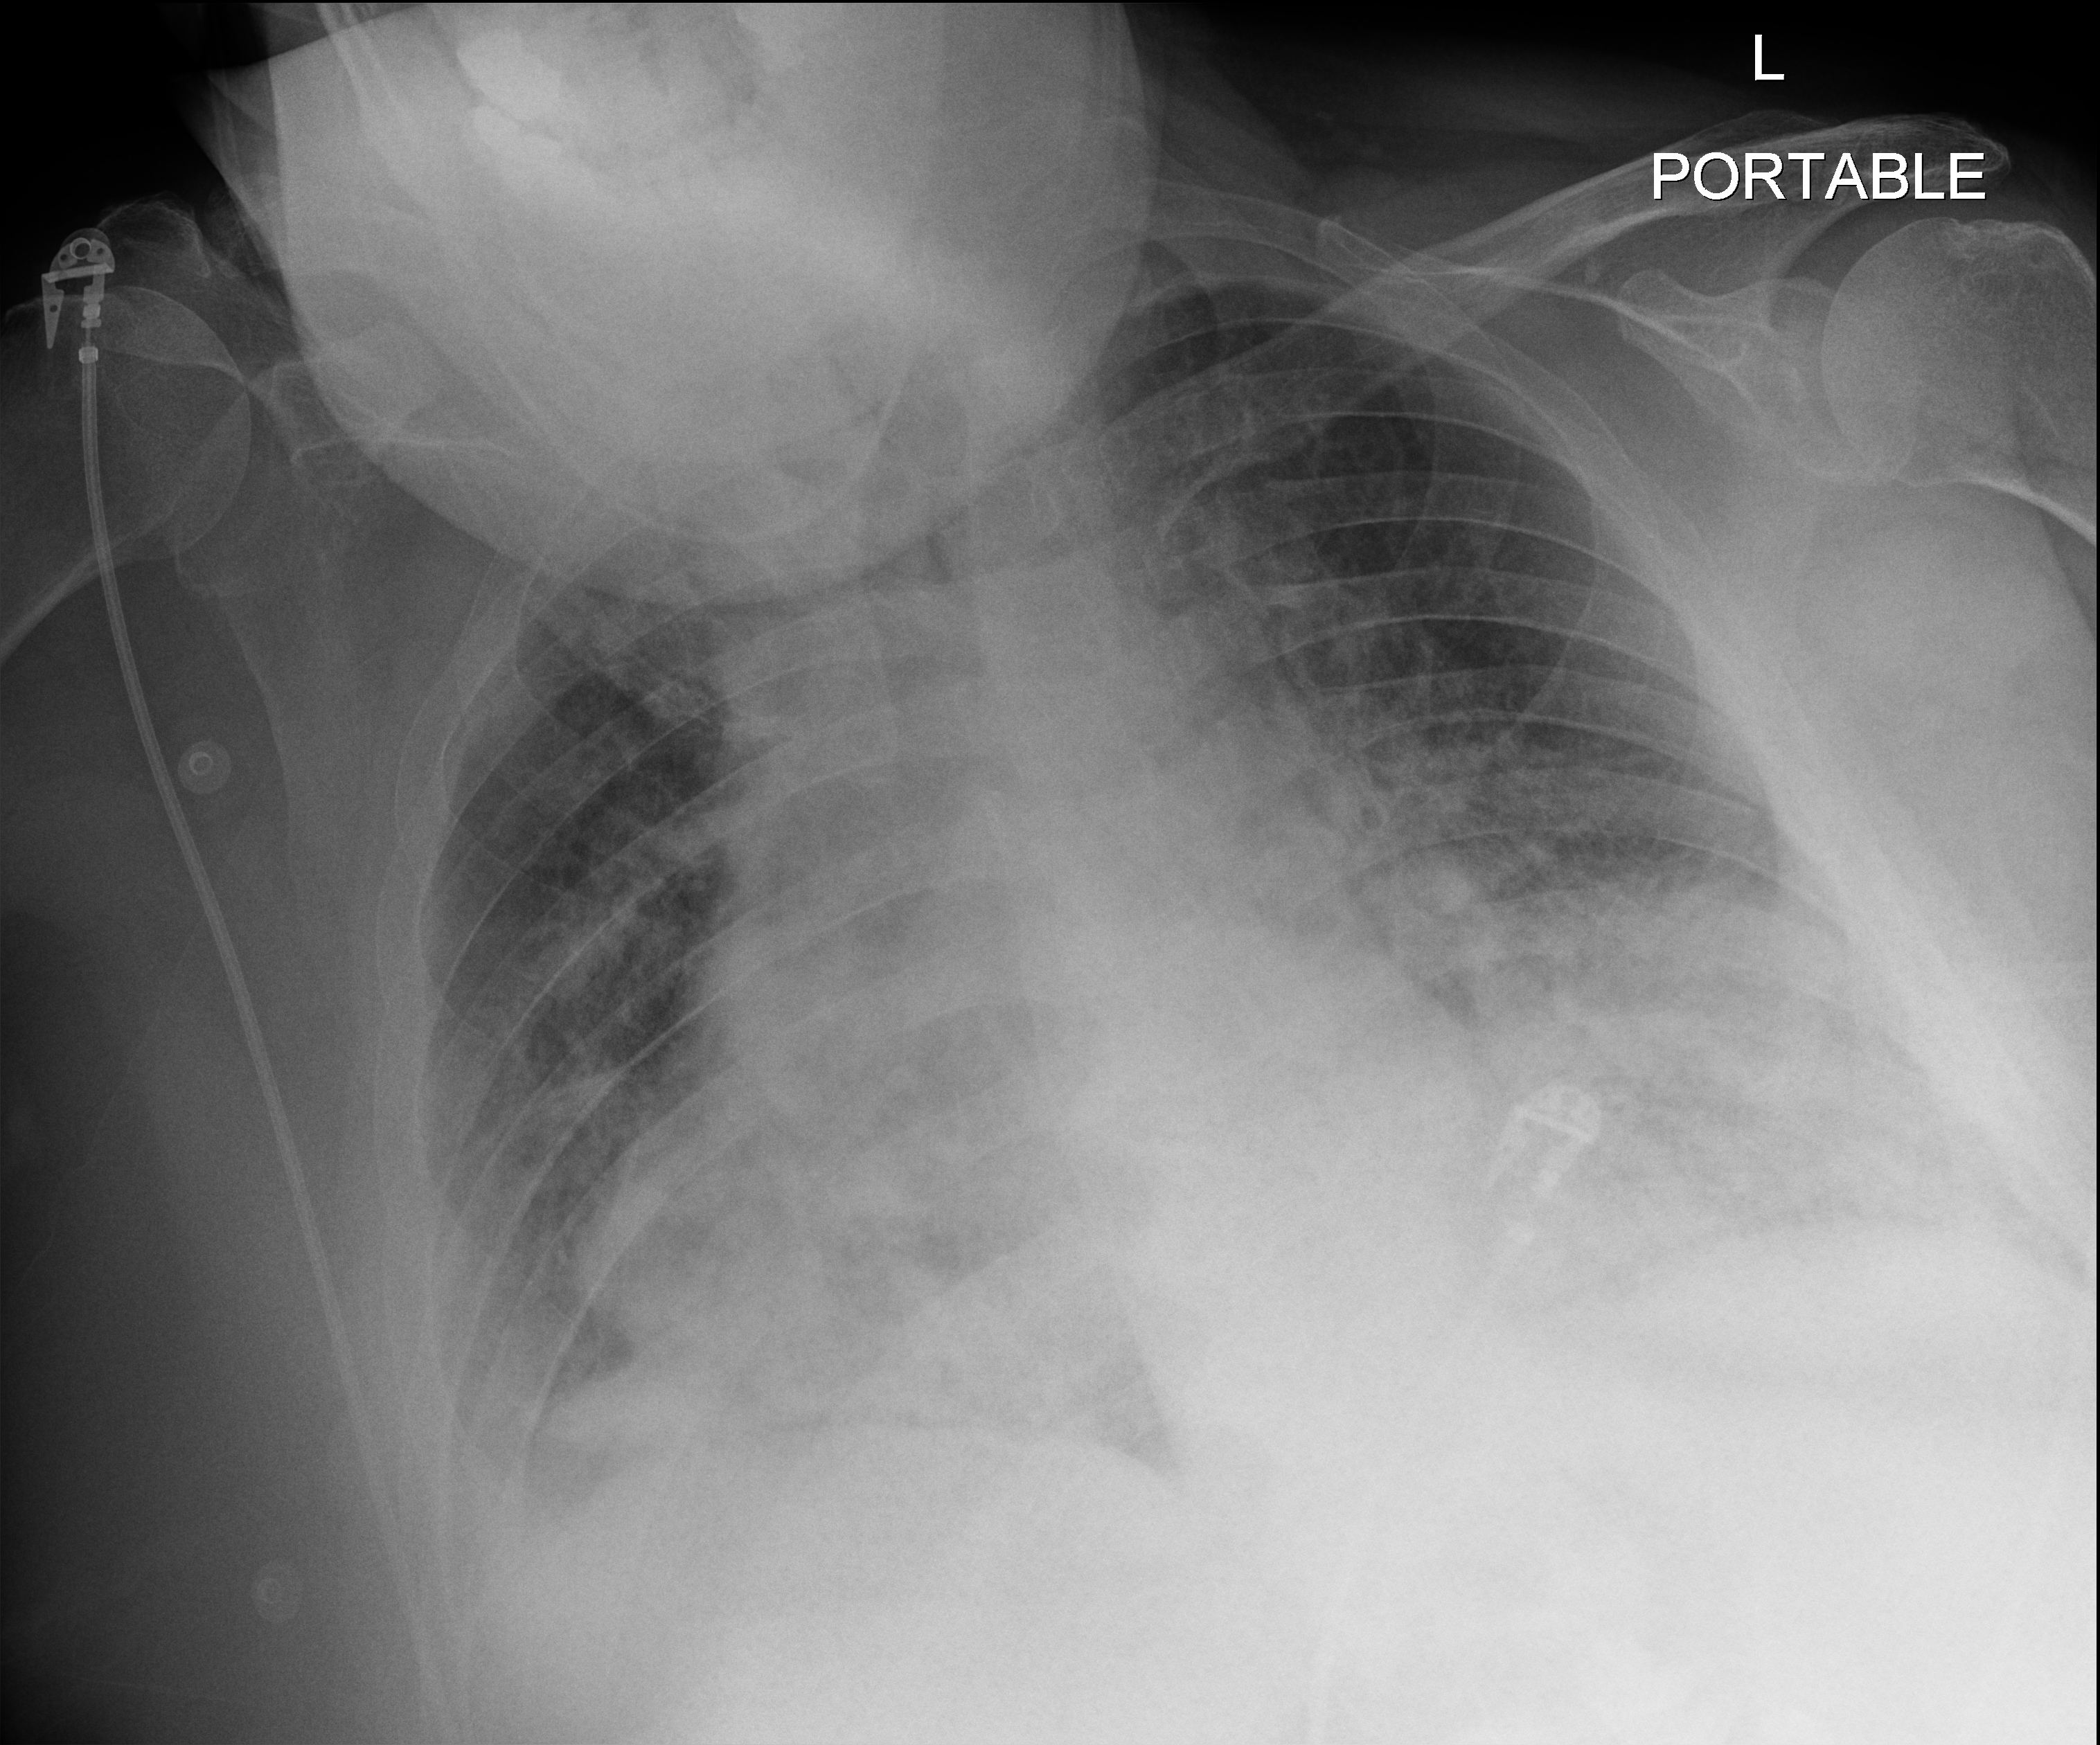
Chest radiograph (digital radiography). Male patient hospitalised with COVID-19, age 60–74 years.
From the hospital-stay record, not from the radiograph (when in the stay this image was taken is not recorded): admitted to intensive care during this hospital stay: yes; mechanically ventilated during this hospital stay: yes; diabetes (admission record): no.